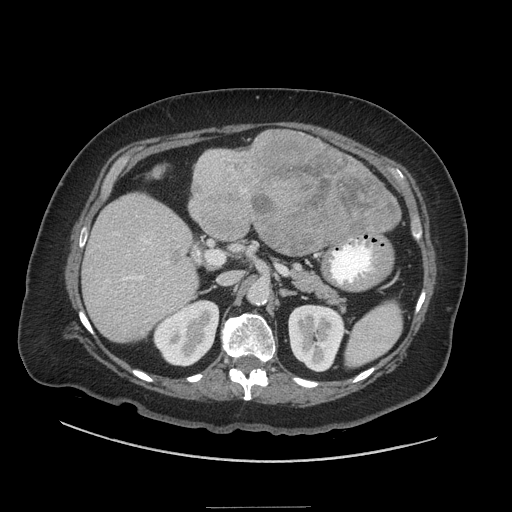
Contrast-enhanced abdominal CT (liver protocol), one axial slice; slice 18 of 81 in the series (ordered by position); reconstruction kernel STANDARD; 140 kVp; soft-tissue window (W 400 / L 40 HU); 512 × 512 image matrix. From the clinical record (not read from this slice): diagnosis: hepatocellular carcinoma (patient treated with transarterial chemoembolisation; whether this scan precedes or follows treatment is not stated here); TNM stage (as recorded): Stage-II; Child-Pugh class: A; tumour nodularity: multinodular; tumour size: 1.7 cm.
Annotated regions visible in this slice (semi-automatic segmentation, software-assisted and operator-edited):
- liver parenchyma outside the tumour (the mass and vessels are separate outlines, so this box may not span the whole liver): bounding box (x1, y1, x2, y2) in pixels: (82, 134, 392, 342)
- mass: (170, 130, 402, 263)
- liver vessels: (106, 233, 179, 294)